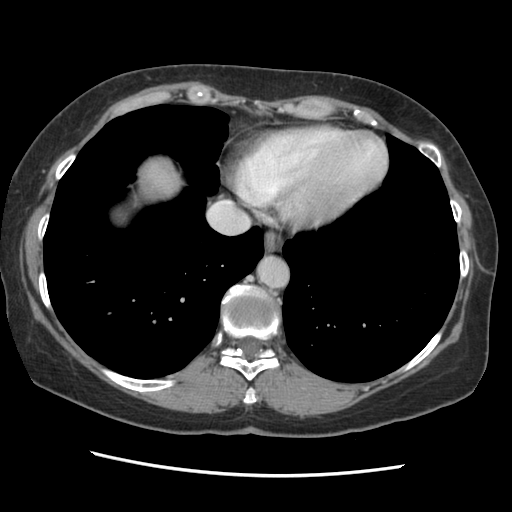
Contrast-enhanced abdominal CT, one axial slice. Slice 127 of 141 in the series (ordered by position). 120 kVp. Soft-tissue window (W 400 / L 40 HU). 512 × 512 image matrix. Female patient, age 61 years. Case-level facts recorded for this patient, not image findings: diagnosis: colorectal cancer liver metastases, imaged before liver resection; multiple liver metastases: no; largest metastasis: 2.4 cm; chemotherapy before resection: no.
Outlined on this slice (expert manual segmentation):
- liver: bounding box <134,155,183,201> (left, top, right, bottom; pixels)
- planned liver remnant (the part of the liver to remain after resection): <135,155,183,202>